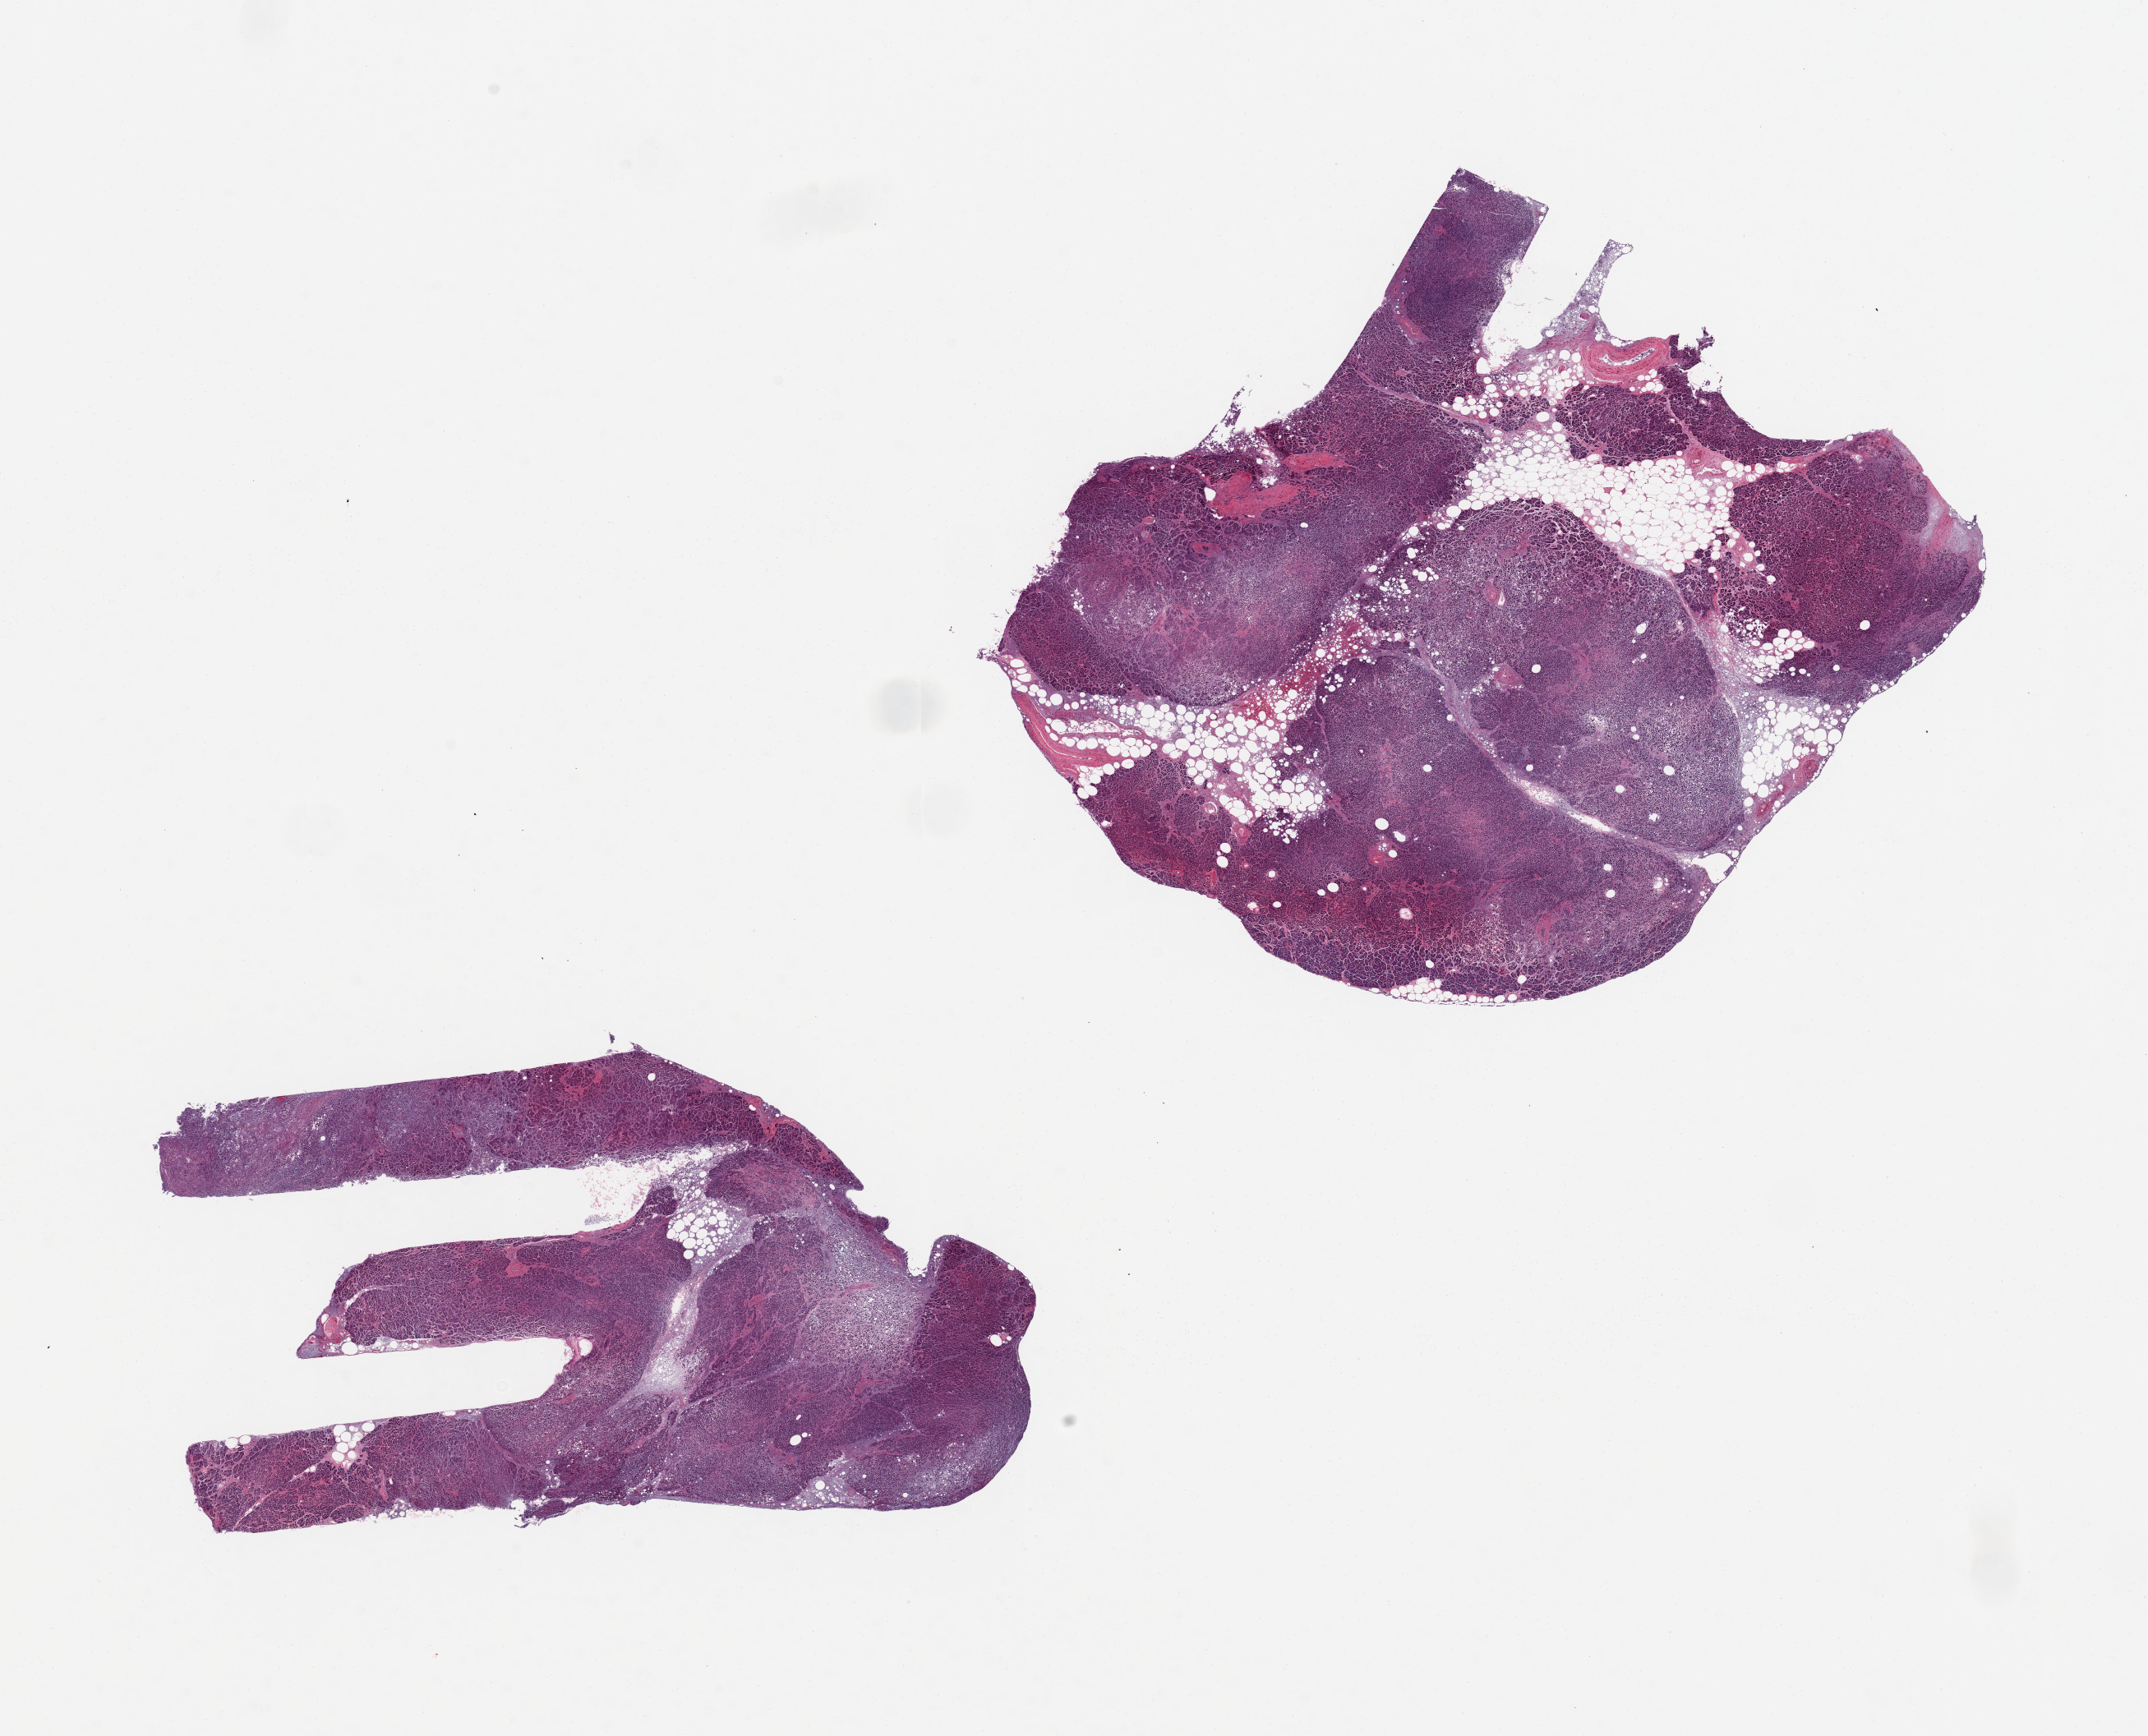
Whole-slide image, hematoxylin and eosin (H&E) stain — shown as a low-resolution overview of the whole scanned area (about 20.7 x 16.7 mm, slide scanned at 20x). PAXgene-fixed, paraffin-embedded tissue. Section of pancreas (target tissue). Tissue donor sample. Donor sex: male.
Review note (as recorded): 2 pieces, moderate-severe autolysis/saponification. Islets not visible.